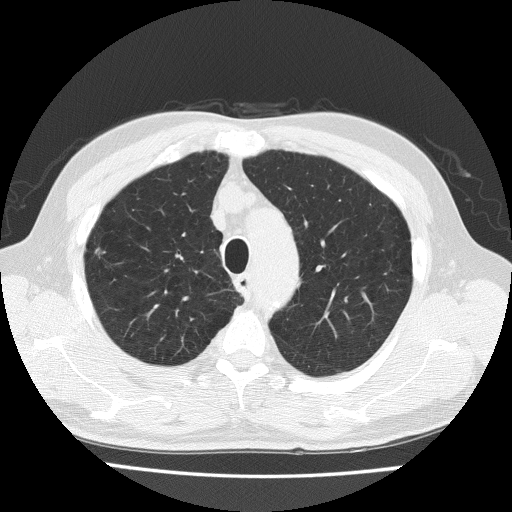
Axial slice from a low-dose chest CT screening exam, baseline annual screen, lung window (W 1500 / L -600 HU), lung (sharp) reconstruction kernel (FC51), 512 × 512 image matrix, field of view 350 × 350 mm. Male participant, aged 73 years at enrolment. Former smoker at enrolment.
- Lesion marked by an expert reader, box from (x=75, y=236) to (x=116, y=273) px.
- Reader record for this screening exam (exam-level; its link to the box is not recorded): non-calcified nodule or mass ≥4 mm, right upper lobe, 4 × 4 mm, spiculated (stellate) margins, soft tissue attenuation.
- Official screen result: positive, change unspecified: nodule(s) >= 4 mm or enlarging nodule(s), mass(es), or other non-specific abnormalities suspicious for lung cancer.
- Participant outcome: lung cancer diagnosed 170 days after this screen — adenocarcinoma, NOS, right upper lobe, poorly differentiated (G3), stage IA (AJCC 6th edition), 60 mm at pathology.